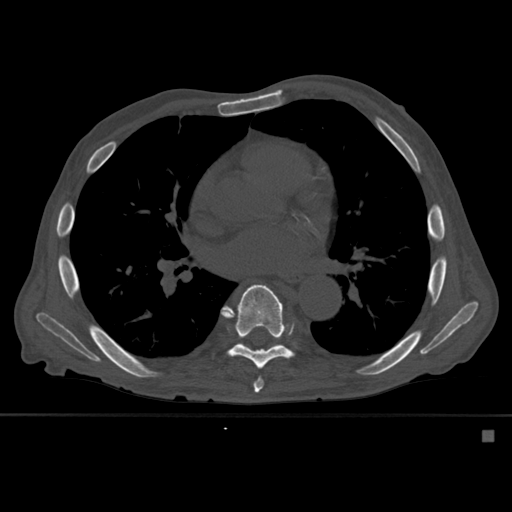
CT including the spine, one axial slice. Position 351 of 527 along the scan axis. Bone window (W 1800 / L 400 HU). 512 × 512 image matrix, field of view 373 × 373 mm. Patient: male, 78 years. From the clinical record (not read from this slice): primary cancer: prostate.
Outlined on this slice (semi-automatically segmented with operator editing):
- T7 vertebra: bounding box (x1, y1, x2, y2) in pixels: (224, 291, 264, 393)
- T8 vertebra: (228, 284, 294, 371)
- T9 vertebra: (237, 337, 280, 351)